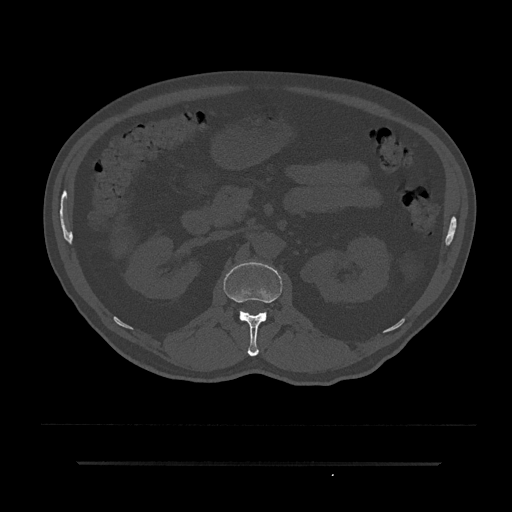
CT including the spine, one axial slice; position 129 of 797 along the scan axis; reconstruction kernel Br40s/3; bone window (W 1800 / L 400 HU); 512 × 512 image matrix, field of view 464 × 464 mm. Male patient, age 59 years. From the clinical record (not read from this slice): primary cancer: bile ducts.
Structures marked on this image (semi-automatically segmented with operator editing):
- L1 vertebra: bounding box [x1, y1, x2, y2] px = [223, 262, 282, 356]